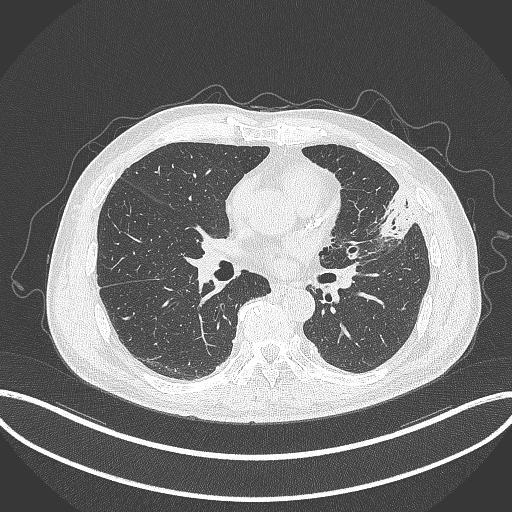
Chest CT, one axial slice. Position 164 of 382 along the scan axis. Lung window (W 1500 / L -600 HU). 512 × 512 image matrix, field of view 415 × 415 mm. Male patient, age 64 years. From the clinical record (not read from this slice): clinical TNM (as recorded): T4 N1 M0.
Annotated regions visible in this slice (bounding box drawn by a radiologist):
- lung tumour (recorded histology: adenocarcinoma): bounding box <373,189,415,244> (left, top, right, bottom; pixels)